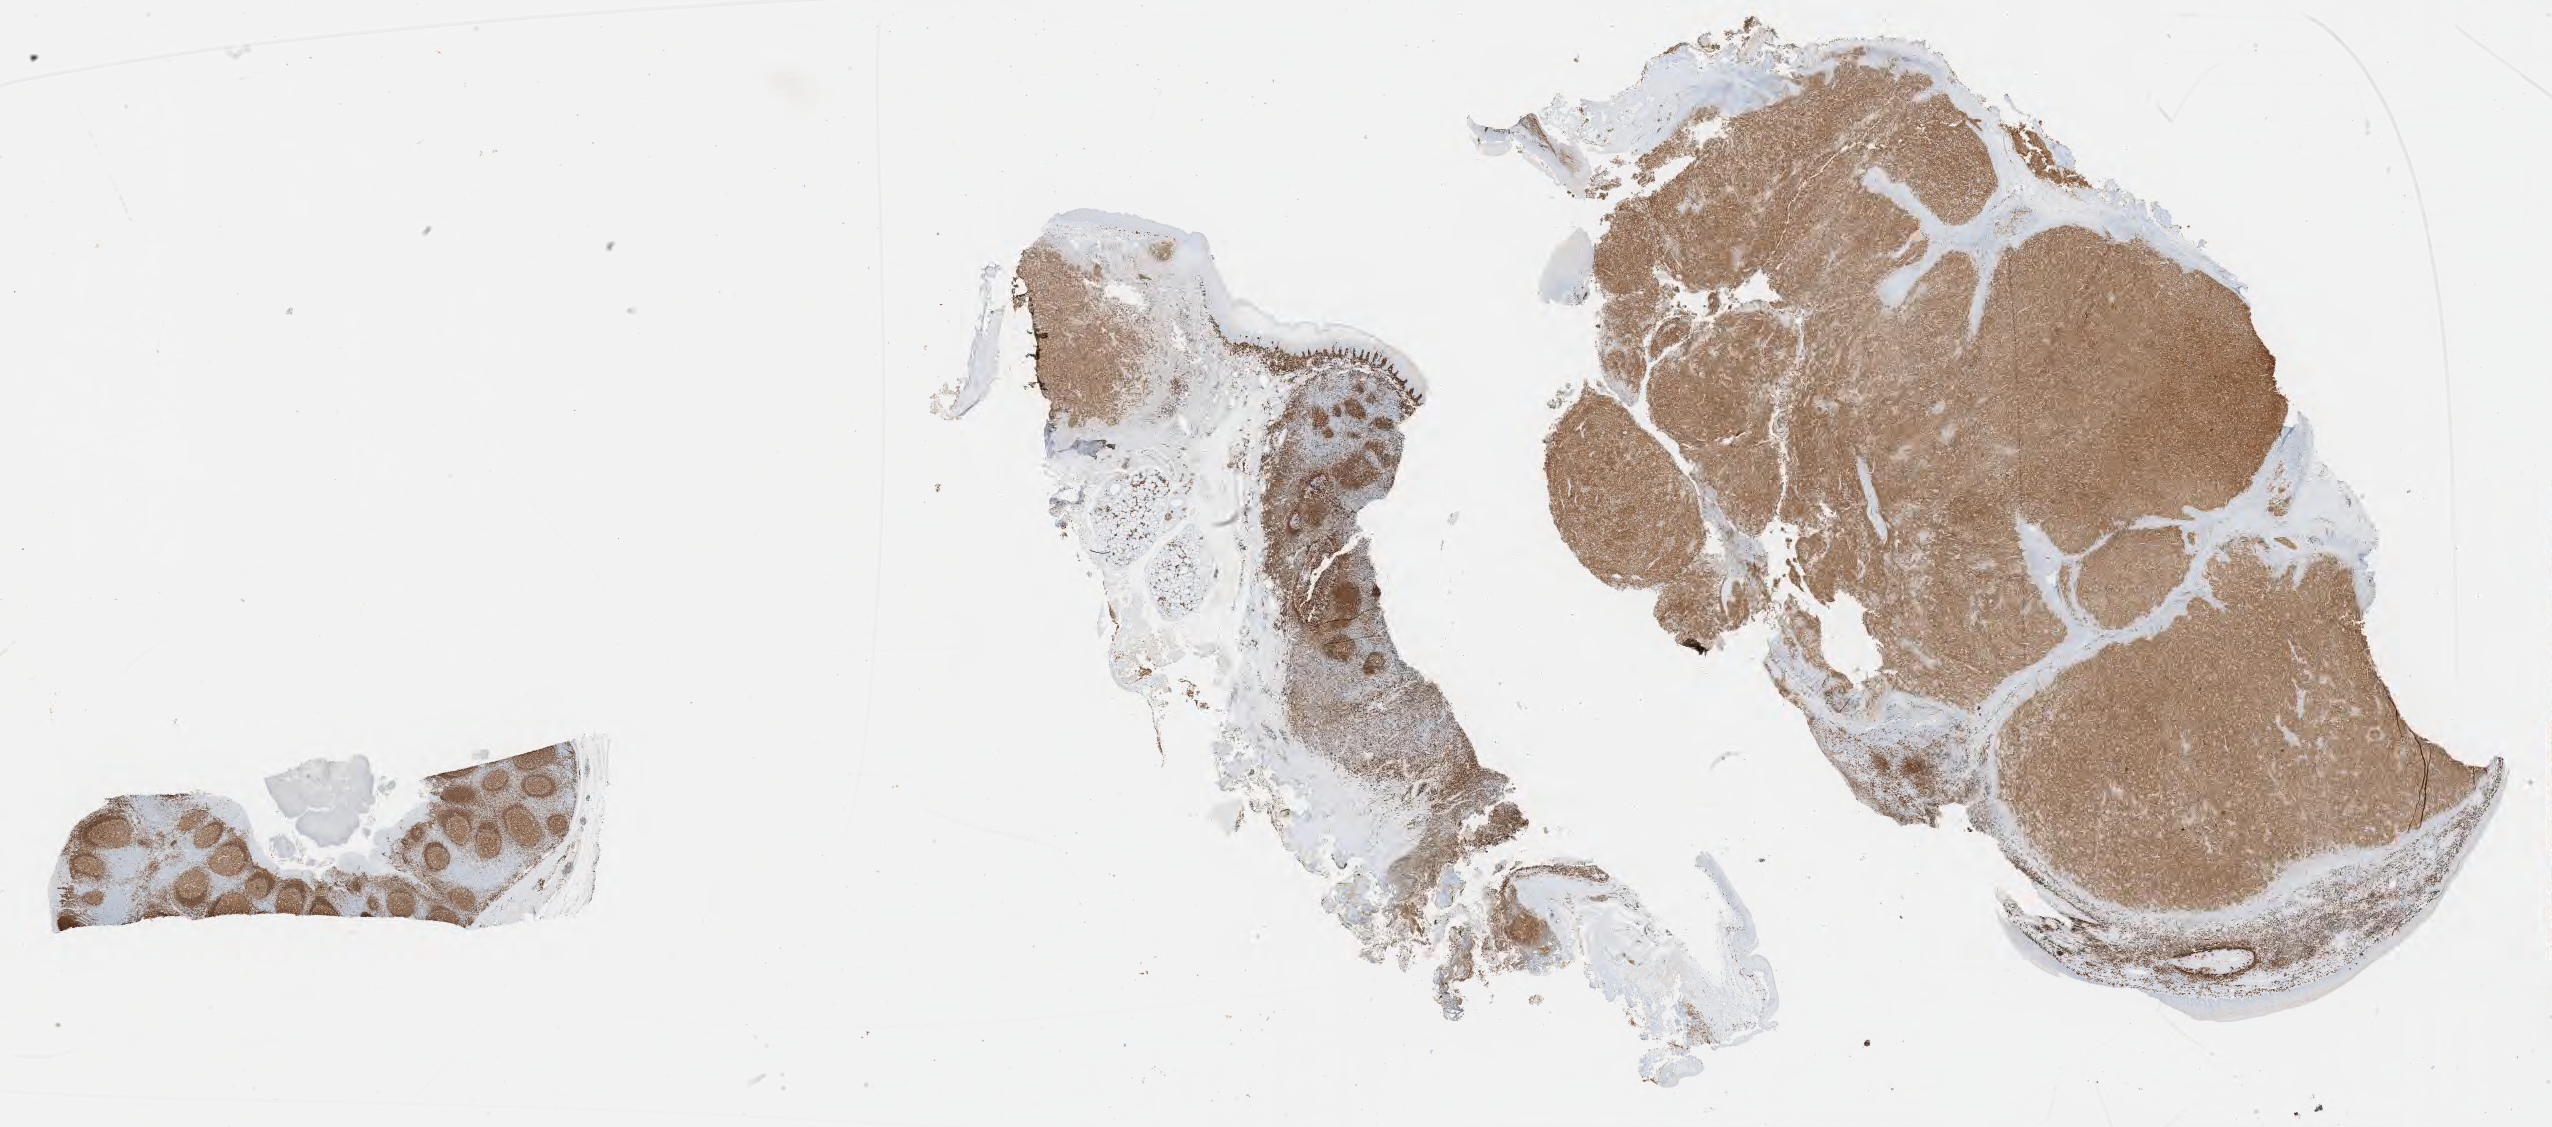
IHC for CD79a, whole-slide image, a low-resolution overview of the entire scanned area, about 41.3 x 18.2 mm; specimen: tumor tissue; site: lymph node. Male patient, age 56 years.
Histologic diagnosis: Diffuse large B-cell lymphoma, NOS.